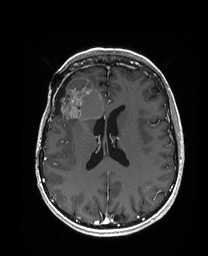
Brain MRI from a brain-tumour surgery series, one axial slice. Position 79 of 192 along the scan axis. T1-weighted post-contrast. 1 mm slice thickness. 208 × 256 image matrix, field of view 203 × 250 mm. Case-level facts recorded for this patient, not image findings: histopathology: Metastatic Carcinoma from Breast primary.
Annotated regions visible in this slice (expert manual segmentation):
- previous resection cavity: bounding box [x1, y1, x2, y2] px = [54, 77, 70, 115]
- tumour: [55, 77, 104, 120]